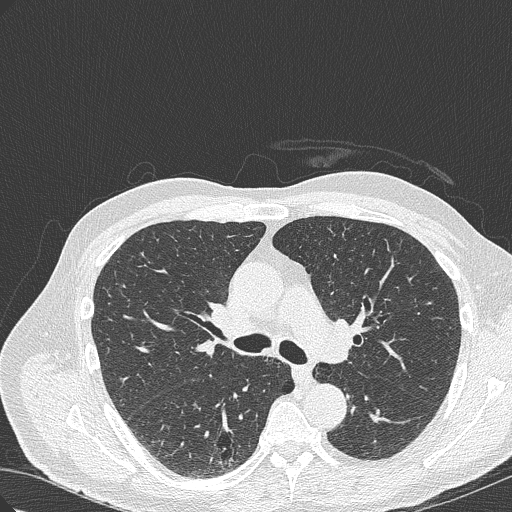
Chest CT (low-dose screening protocol), one axial image, baseline annual screen, lung window (W 1500 / L -600 HU), 1 mm slice thickness, lung (sharp) reconstruction kernel (B50f), slice 119 of 322 in the series. Male participant, aged 70 years at enrolment. Current smoker at enrolment.
Expert-annotated lung lesion, bounding box <200,419,264,469> (left, top, right, bottom; pixels). The screening reader recorded 4 non-calcified nodules or masses ≥4 mm on this exam; which of them this box marks is not recorded. Later outcome: lung cancer diagnosed 978 days after this screen (after the third annual screen) — bronchiolo-alveolar adenocarcinoma, NOS, right lower lobe, poorly differentiated (G3), stage IB (AJCC 6th edition), 30 mm at pathology.